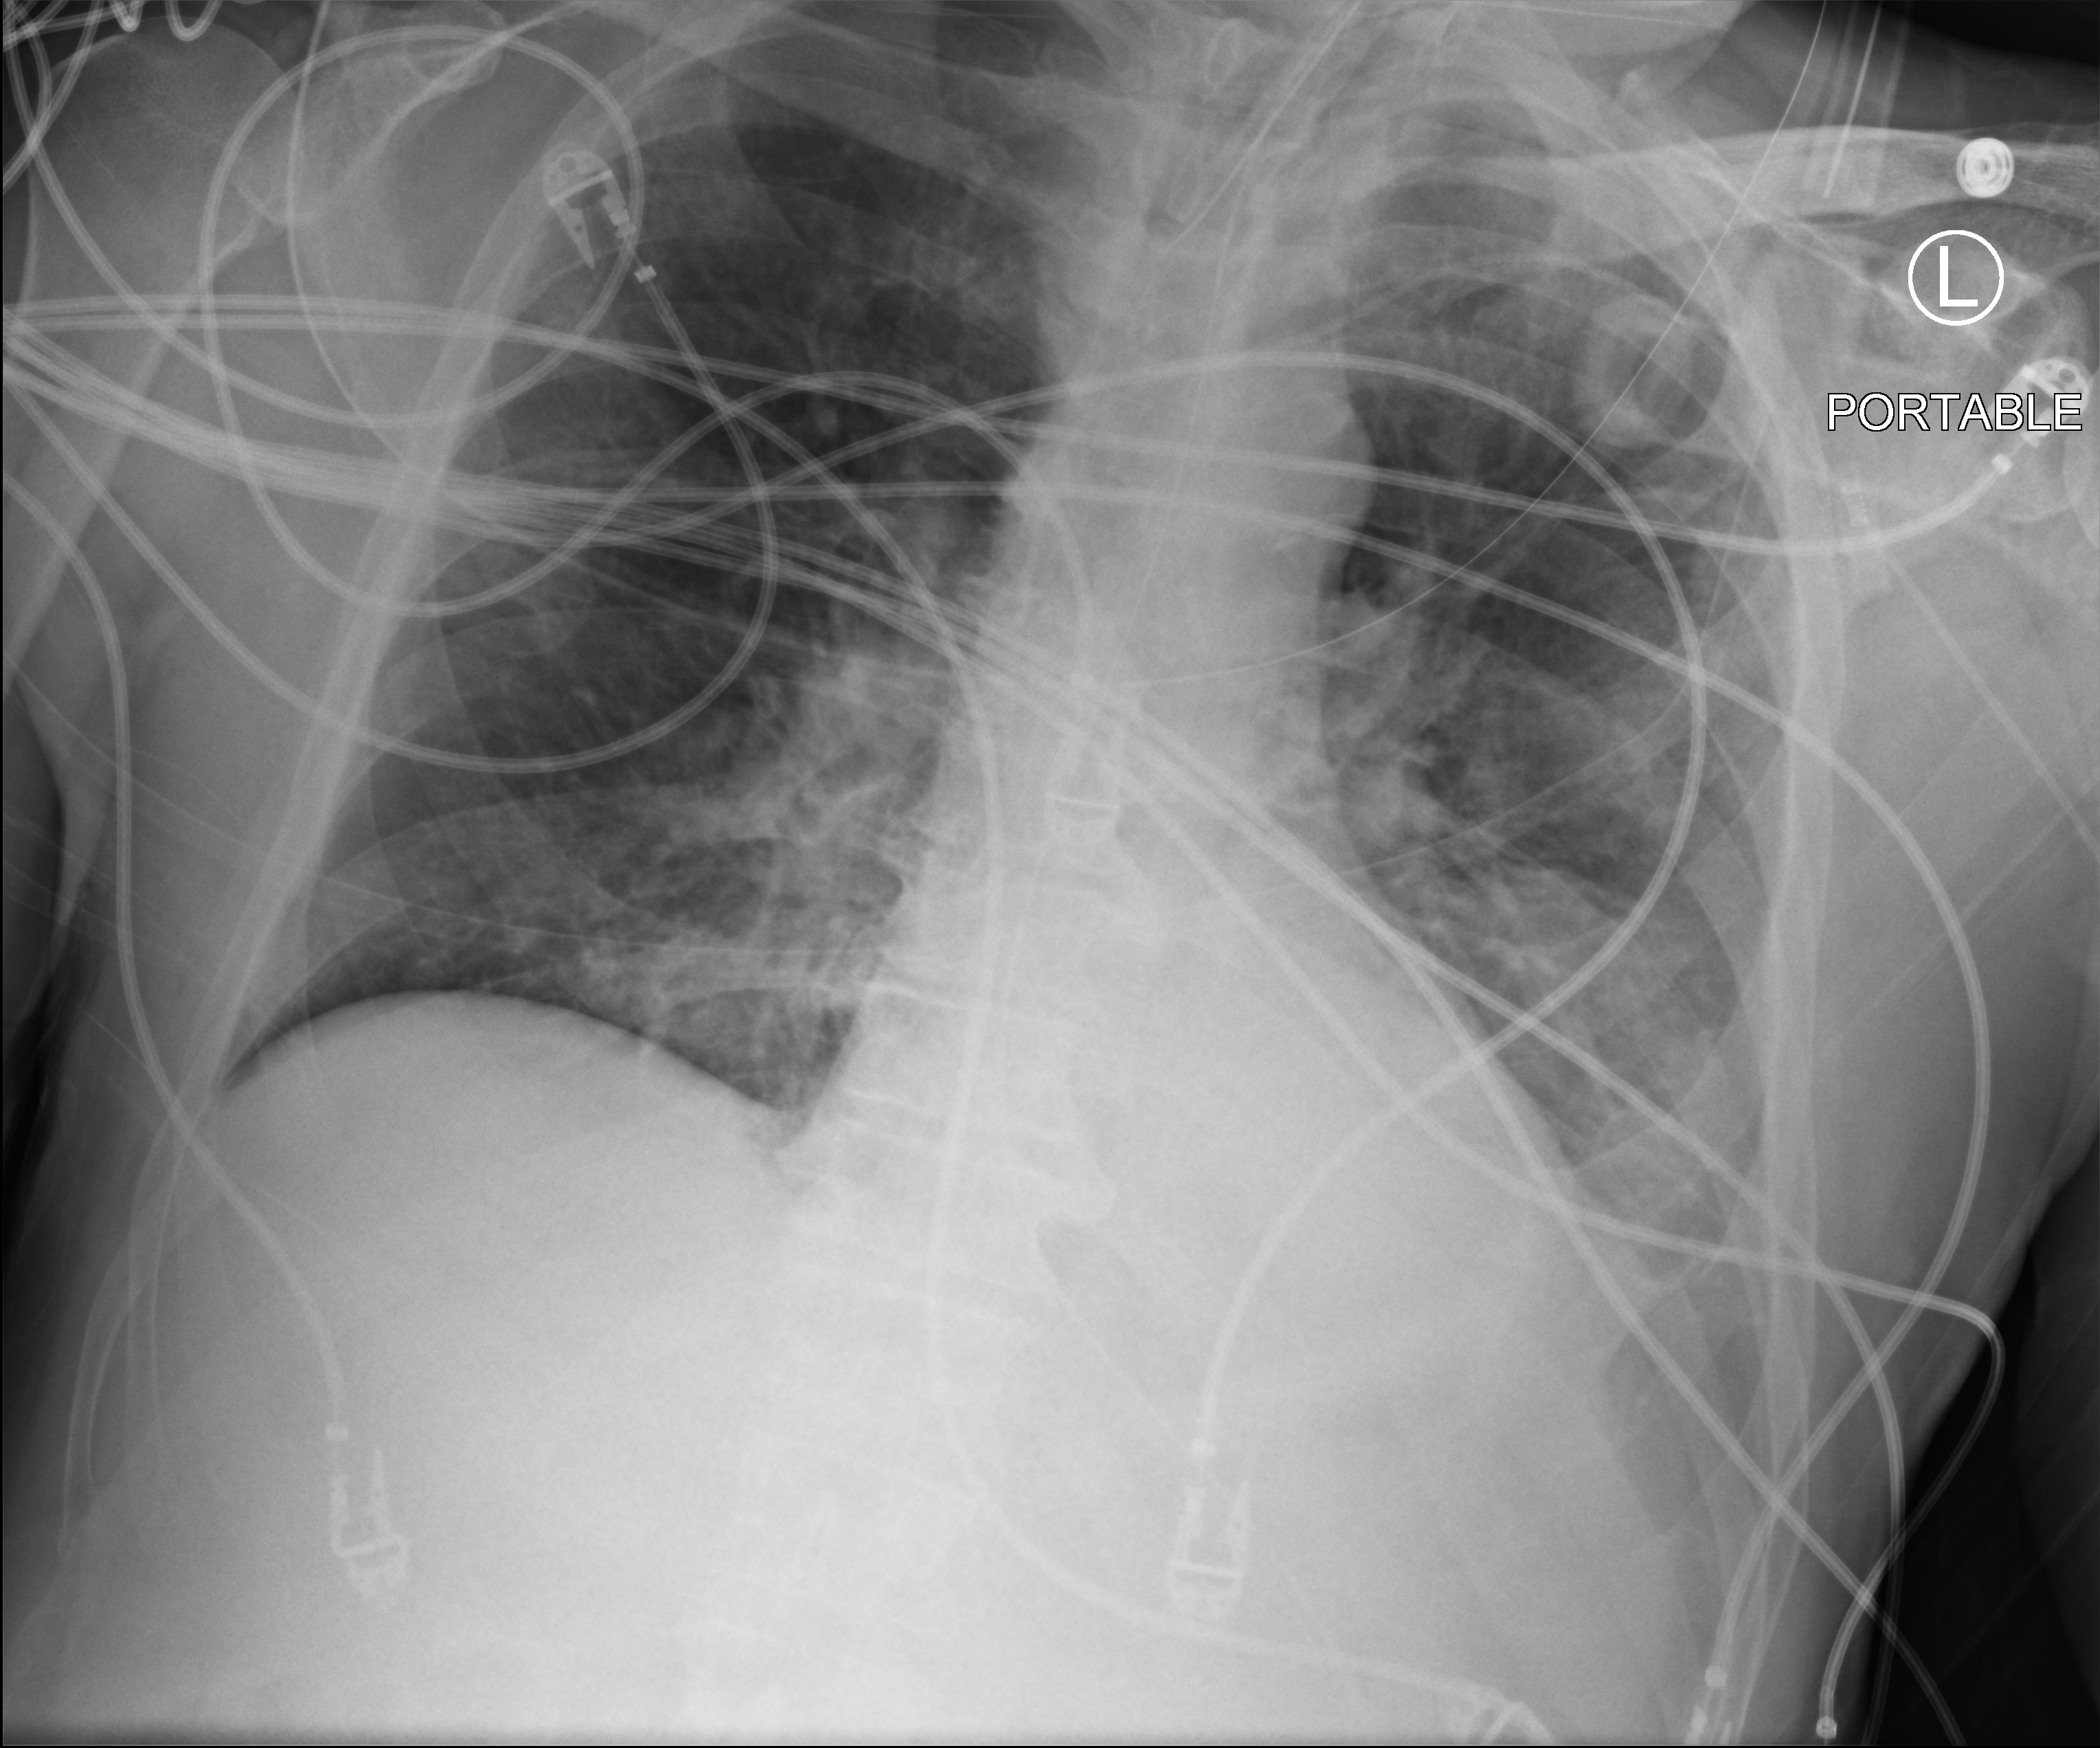
Bedside chest radiograph (computed radiography); anteroposterior (AP) projection. Patient hospitalised with COVID-19; male, aged 60–74 years.
Hospital-stay facts (about this admission, not read from this image; timing relative to this image not recorded): admitted to intensive care during this hospital stay: yes.